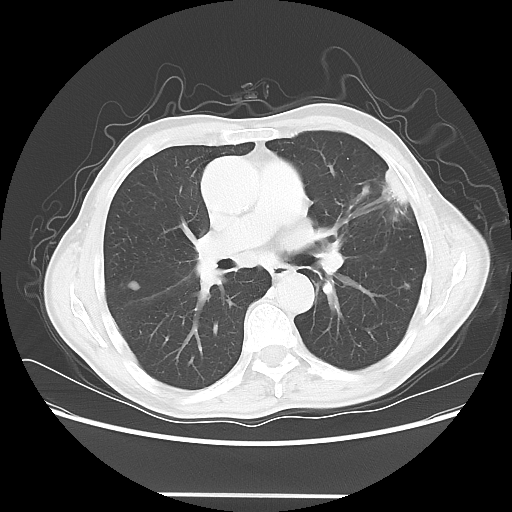
Chest CT, one axial slice; slice 36 of 64 in the series (ordered by position); reconstruction kernel LUNG; 120 kVp; lung window (W 1500 / L -600 HU); 5 mm slice thickness; 512 × 512 image matrix. Male patient, age 71 years. From the clinical record (not read from this slice): clinical TNM (as recorded): T1c N0 M0; histopathological grade: G2-3.
Structures marked on this image (rectangle marked by the reading radiologist):
- lung tumour (recorded histology: adenocarcinoma): bounding box (x1, y1, x2, y2) in pixels: (374, 155, 416, 224)